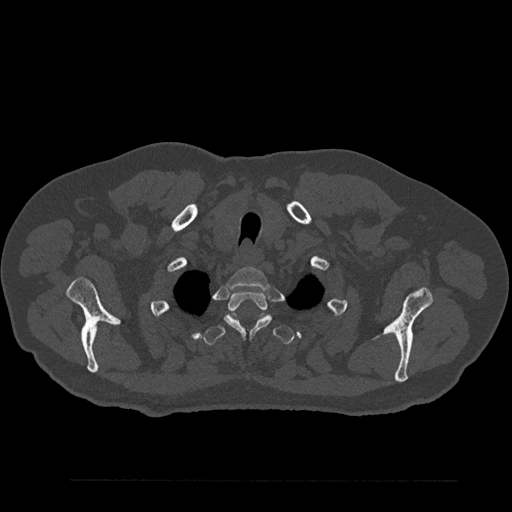
CT including the spine, one axial slice; slice 714 of 797 in the series (ordered by position); reconstruction kernel Br40s/3; 120 kVp; bone window (W 1800 / L 400 HU); 0.5 mm slice thickness; 512 × 512 image matrix, field of view 430 × 430 mm. Patient: male, 61 years. Case-level facts recorded for this patient, not image findings: primary cancer: prostate.
Annotated regions visible in this slice (semi-automatically segmented with operator editing):
- T1 vertebra: bounding box (x1, y1, x2, y2) in pixels: (227, 267, 270, 289)
- T2 vertebra: (224, 291, 272, 338)
- T3 vertebra: (204, 313, 294, 345)